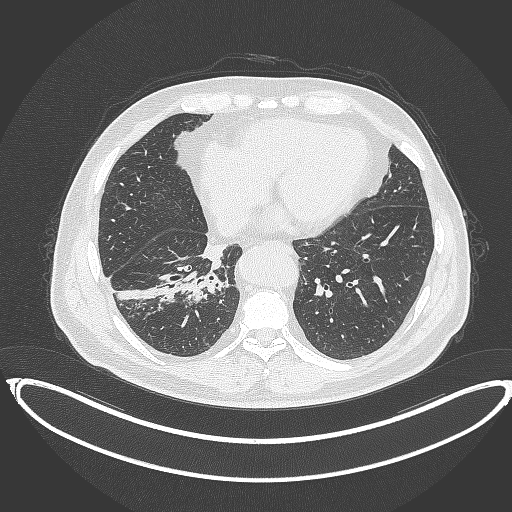
Chest CT, one axial slice. Slice 141 of 387 in the series (ordered by position). 120 kVp. Lung window (W 1500 / L -600 HU). 1 mm slice thickness. 512 × 512 image matrix. Male patient, age 61 years. From the clinical record (not read from this slice): clinical TNM (as recorded): T1b N1 M0.
Annotated regions visible in this slice (bounding box drawn by a radiologist):
- lung tumour (recorded histology: squamous cell carcinoma): bounding box <176,270,225,304> (left, top, right, bottom; pixels)